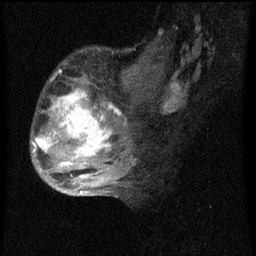
Breast MRI (dynamic contrast-enhanced), one sagittal slice; slice 24 of 60 in the series (ordered by position); dynamic contrast-enhanced series, image 2 of 4 at this slice position (ordered by acquisition); 1.5 T; TE 4.2 ms, TR 8 ms; 2 mm slice thickness; 256 × 256 image matrix. Patient: female, 50 years.
Outlined on this slice (semi-automatic segmentation, software-assisted and operator-edited):
- analysis volume of interest (the breast-tissue region the enhancement analysis was run in; not a lesion): bounding box [x1, y1, x2, y2] px = [31, 50, 124, 177]
- tumour enhancement mask (voxels above the 70 % enhancement threshold inside the analysis volume of interest): [33, 88, 123, 167]